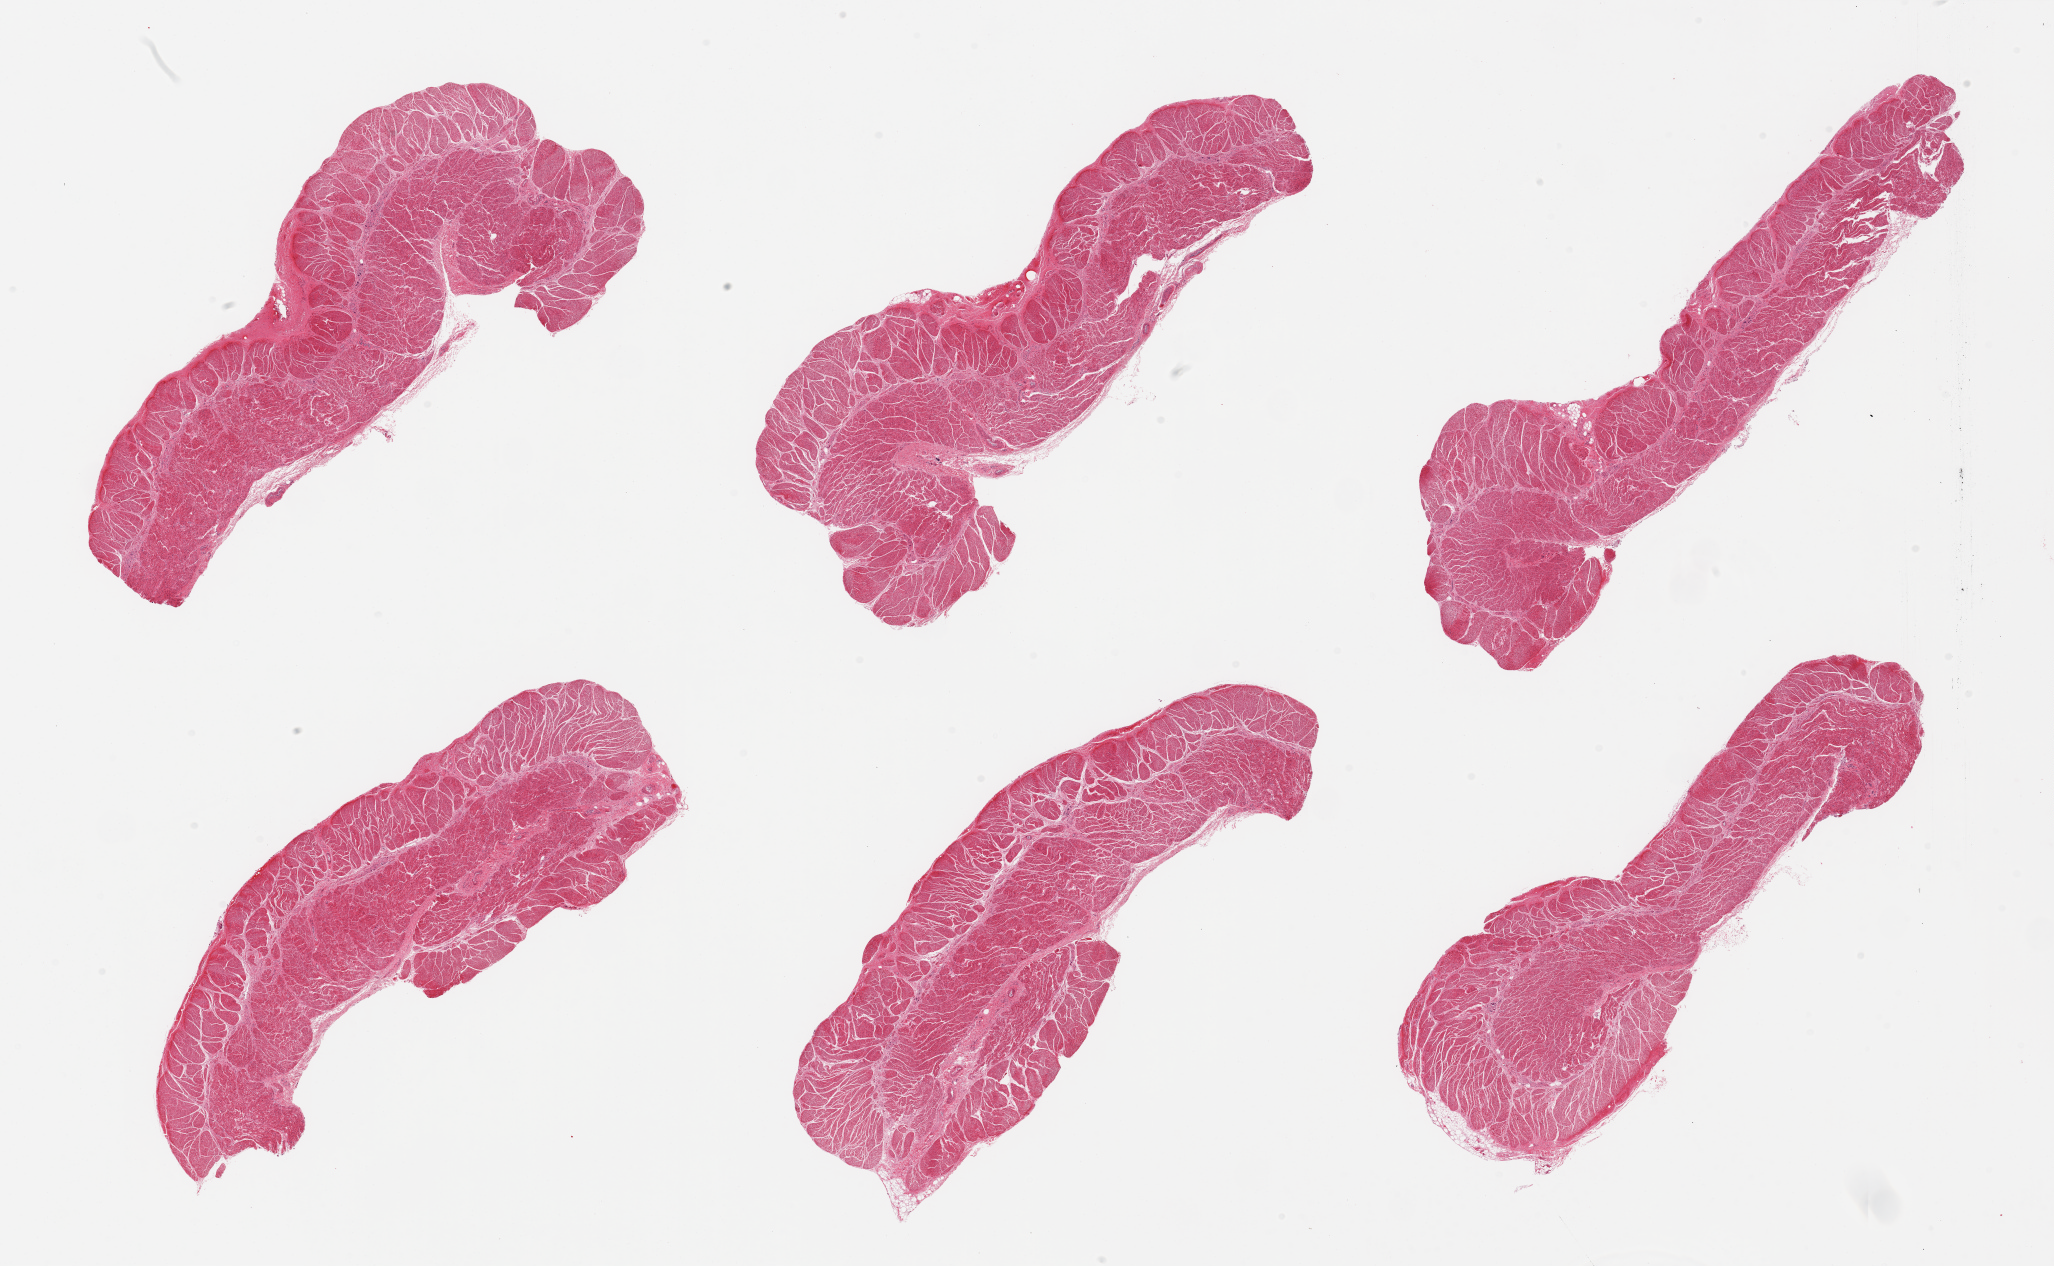
Digitized hematoxylin and eosin (H&E)-stained section, low-resolution overview of the scanned area, about 32.5 x 20.0 mm; PAXgene-fixed, paraffin-embedded tissue; target tissue: esophageal muscle; tissue donor sample.
• reviewer comment on this tissue sample: 6 pieces; well trimmed